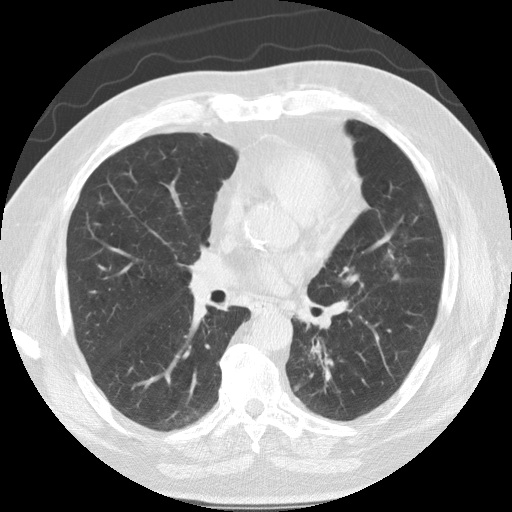
Low-dose screening chest CT, one axial slice; slice 63 of 124 in the series (ordered by position); 120 kVp; lung window (W 1500 / L -600 HU); 2.5 mm slice thickness; 512 × 512 image matrix, field of view 360 × 360 mm.
Outlined on this slice (expert manual segmentation):
- lesion 1 (tumor, lower lobe of left lung): box from (x=310, y=342) to (x=322, y=360) px